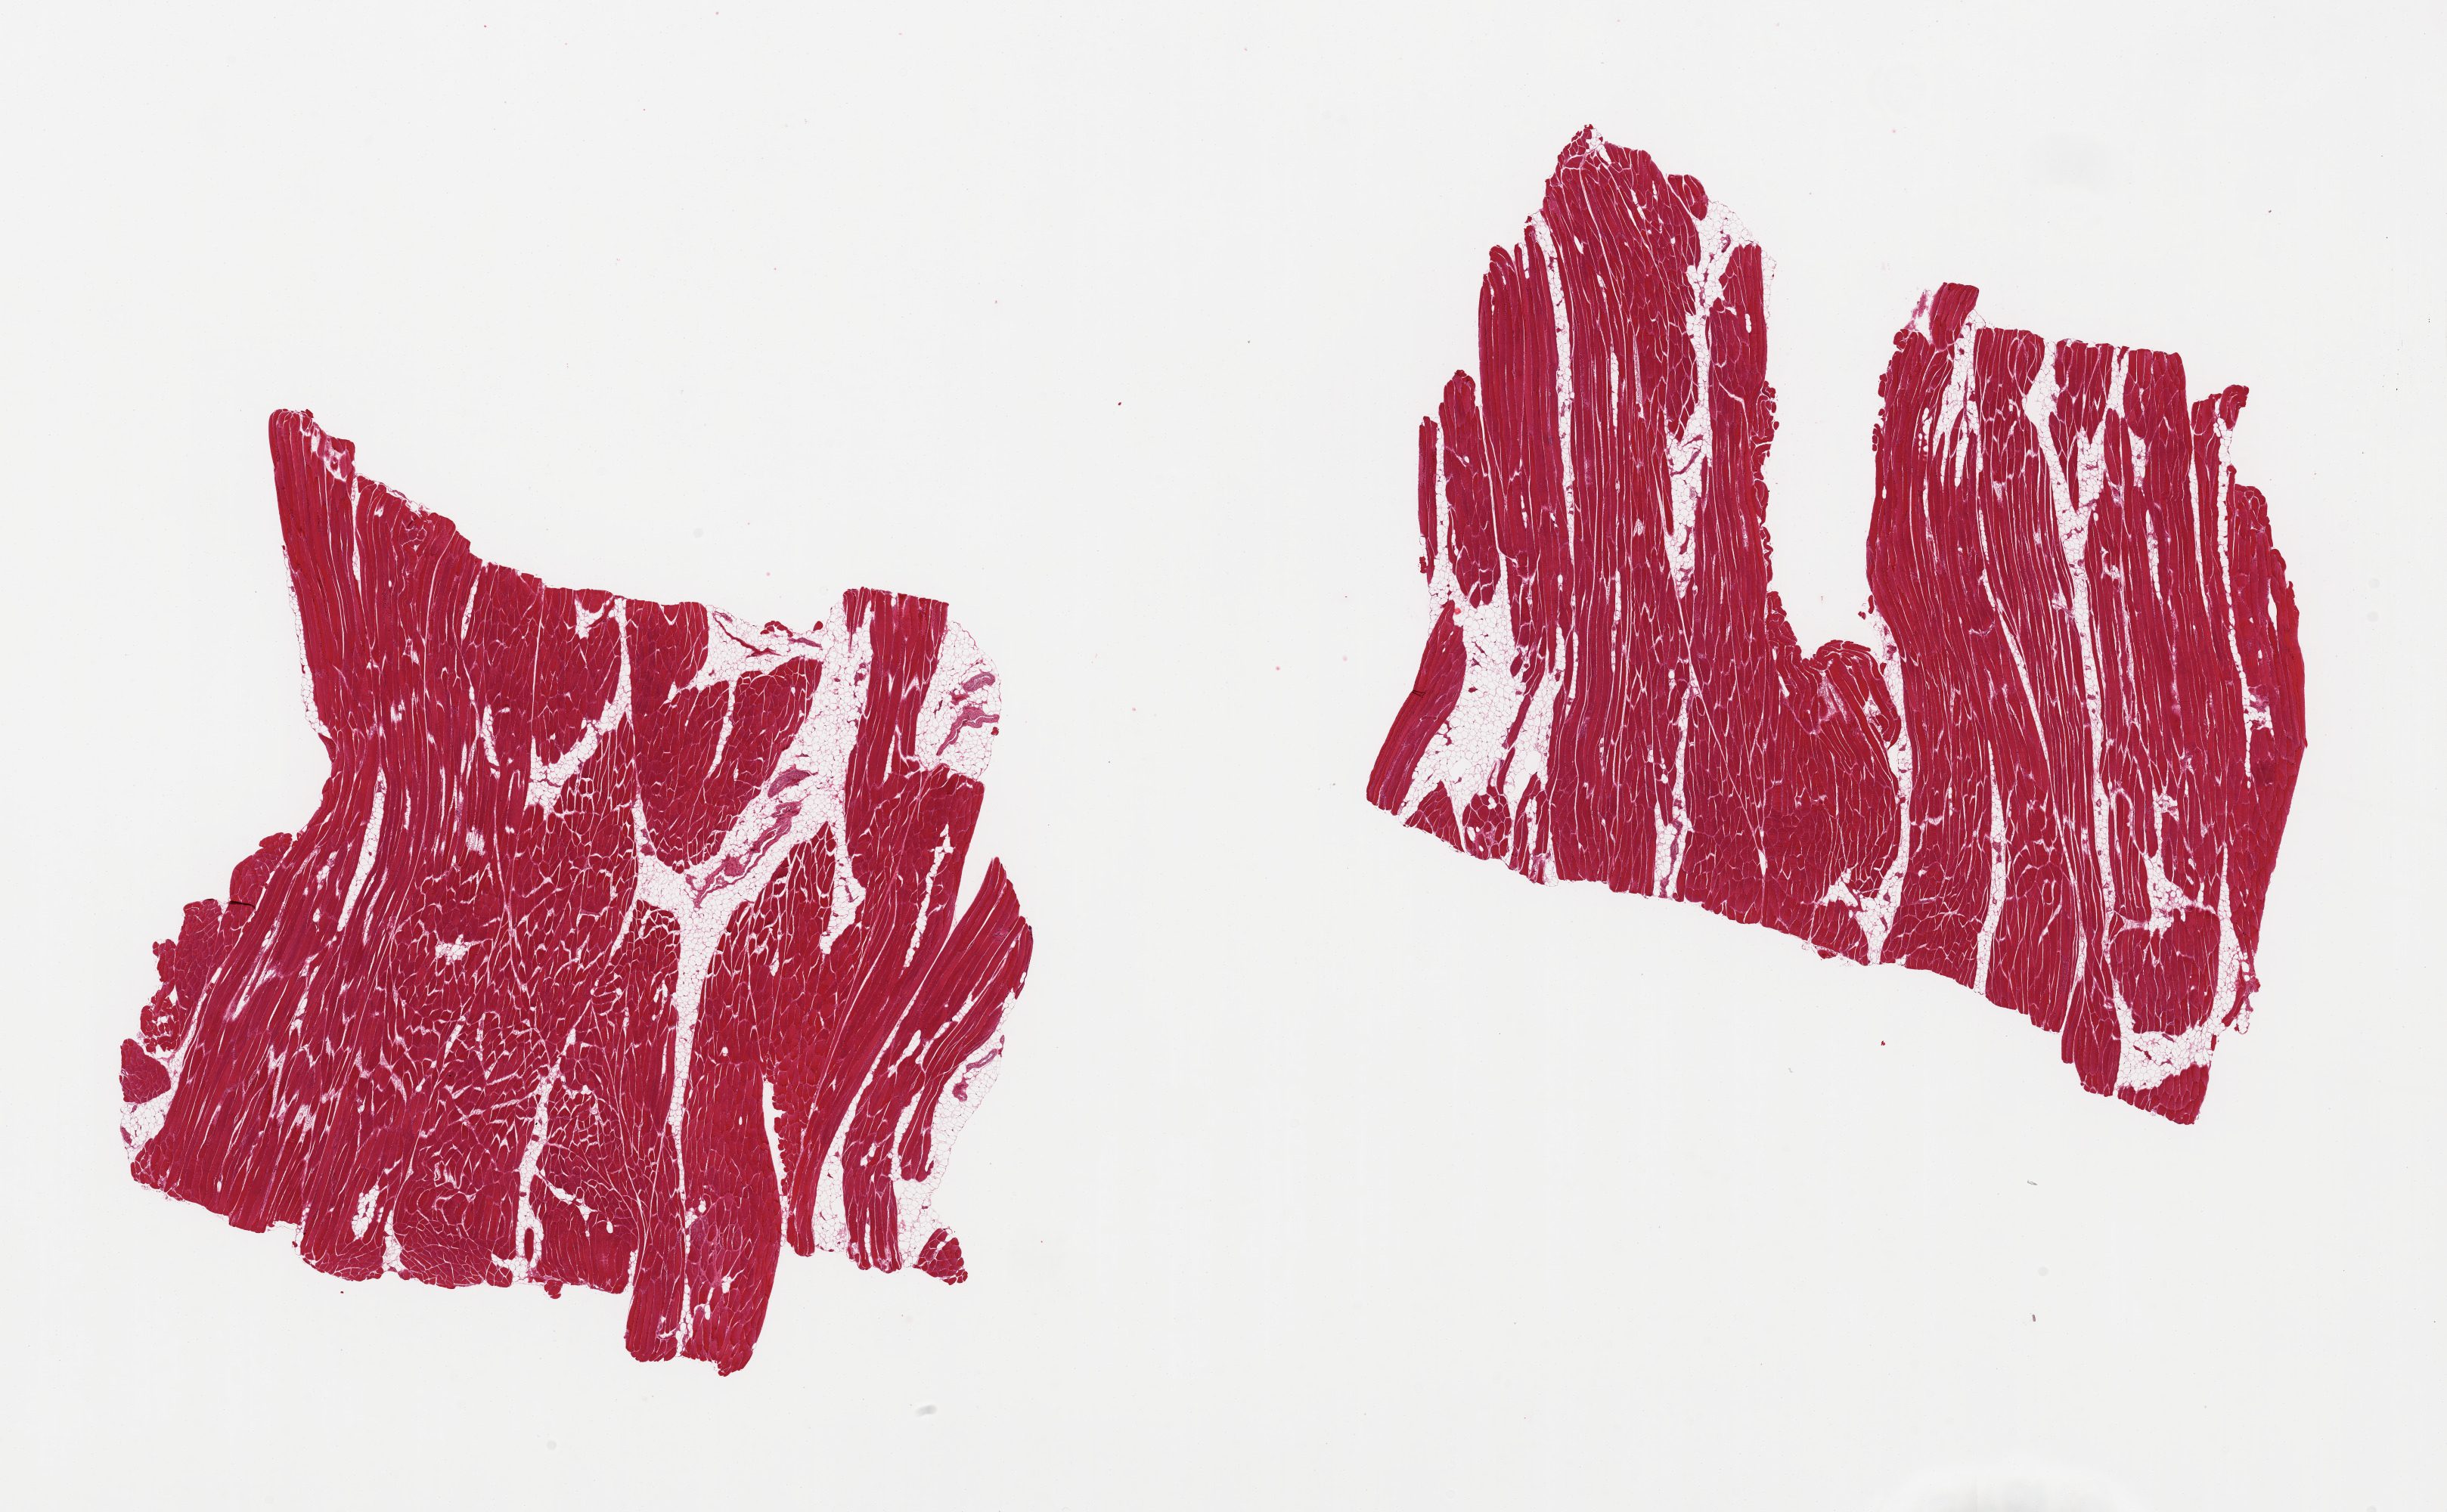
Whole-slide image, hematoxylin and eosin (H&E) stain — shown as a low-resolution overview of the whole scanned area (about 25.6 x 15.8 mm), PAXgene-fixed paraffin-embedded (PFPE) section, sampled site (target tissue): skeletal muscle, donor tissue sample. Donor sex: male.
Review note (as recorded): 2 pieces, ~10% interstitial fat; delinated.